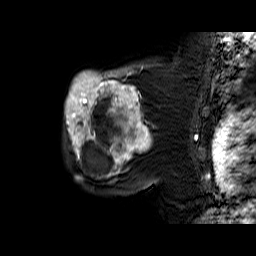
Breast MRI (dynamic contrast-enhanced), one sagittal slice. Position 46 of 60 along the scan axis. Dynamic contrast-enhanced series, time point 2 of 6 at this slice position (early post-contrast). 1.5 T. TE 6.4 ms, TR 32.9 ms. 256 × 256 image matrix. Female patient. Case-level facts recorded for this patient, not image findings: setting: breast cancer imaged before/during neoadjuvant chemotherapy; receptor status: triple-negative.
Outlined on this slice (semi-automatically segmented with operator editing):
- analysis volume of interest (the breast-tissue region the enhancement analysis was run in; not a lesion): bounding box <64,65,159,174> (left, top, right, bottom; pixels)
- tumour enhancement mask (voxels above the 100 % enhancement threshold inside the analysis volume of interest): <65,65,152,174>